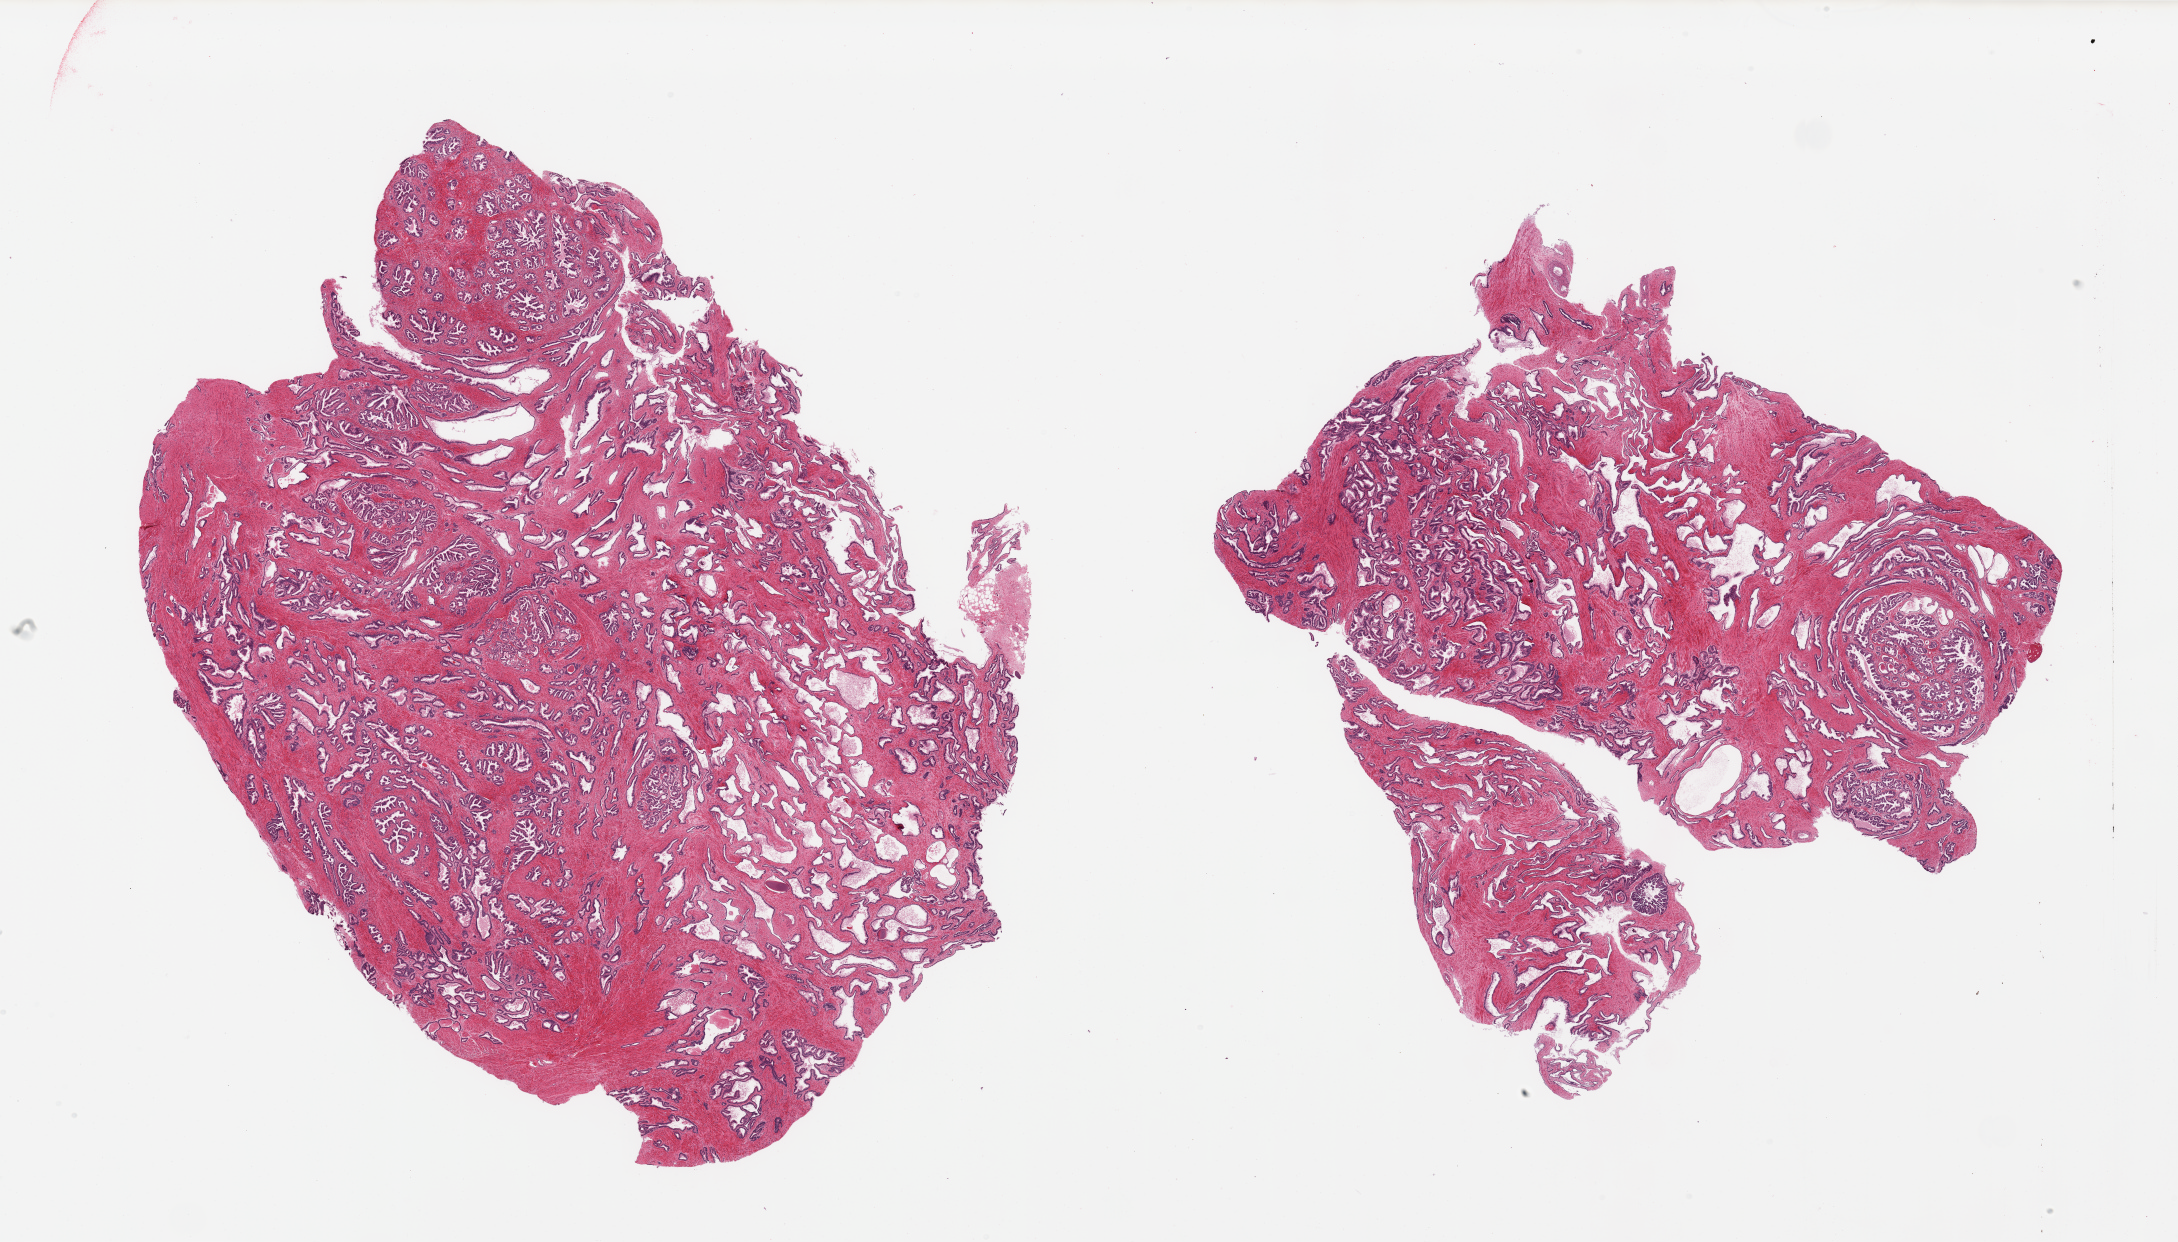
Haematoxylin and eosin whole-slide image, whole scanned area (about 34.5 x 19.6 mm) shown as a low-resolution overview. PAXgene-fixed, paraffin-embedded tissue. Section of prostate (target tissue). Donor tissue sample. Donor sex: male.
• reviewer comment on this tissue sample: 2 pieces, hyperplastic glandular pattern